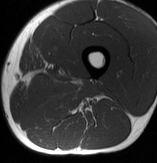
MRI of an extremity soft-tissue mass, one axial slice; position 24 of 70 along the scan axis; MR volume resampled by the dataset authors to the PET/CT grid (not the native acquisition matrix); 3.27 mm slice thickness; 157 × 163 image matrix, field of view 153 × 159 mm. Male patient. From the clinical record (not read from this slice): histological type: extraskeletal osteosarcoma; grade: high; site of the primary tumour: left adductur.
Annotated regions visible in this slice (expert contour drawn on MRI and transferred to this co-registered scan by the dataset authors):
- gross tumour volume (mass): bounding box <26,74,102,105> (left, top, right, bottom; pixels)